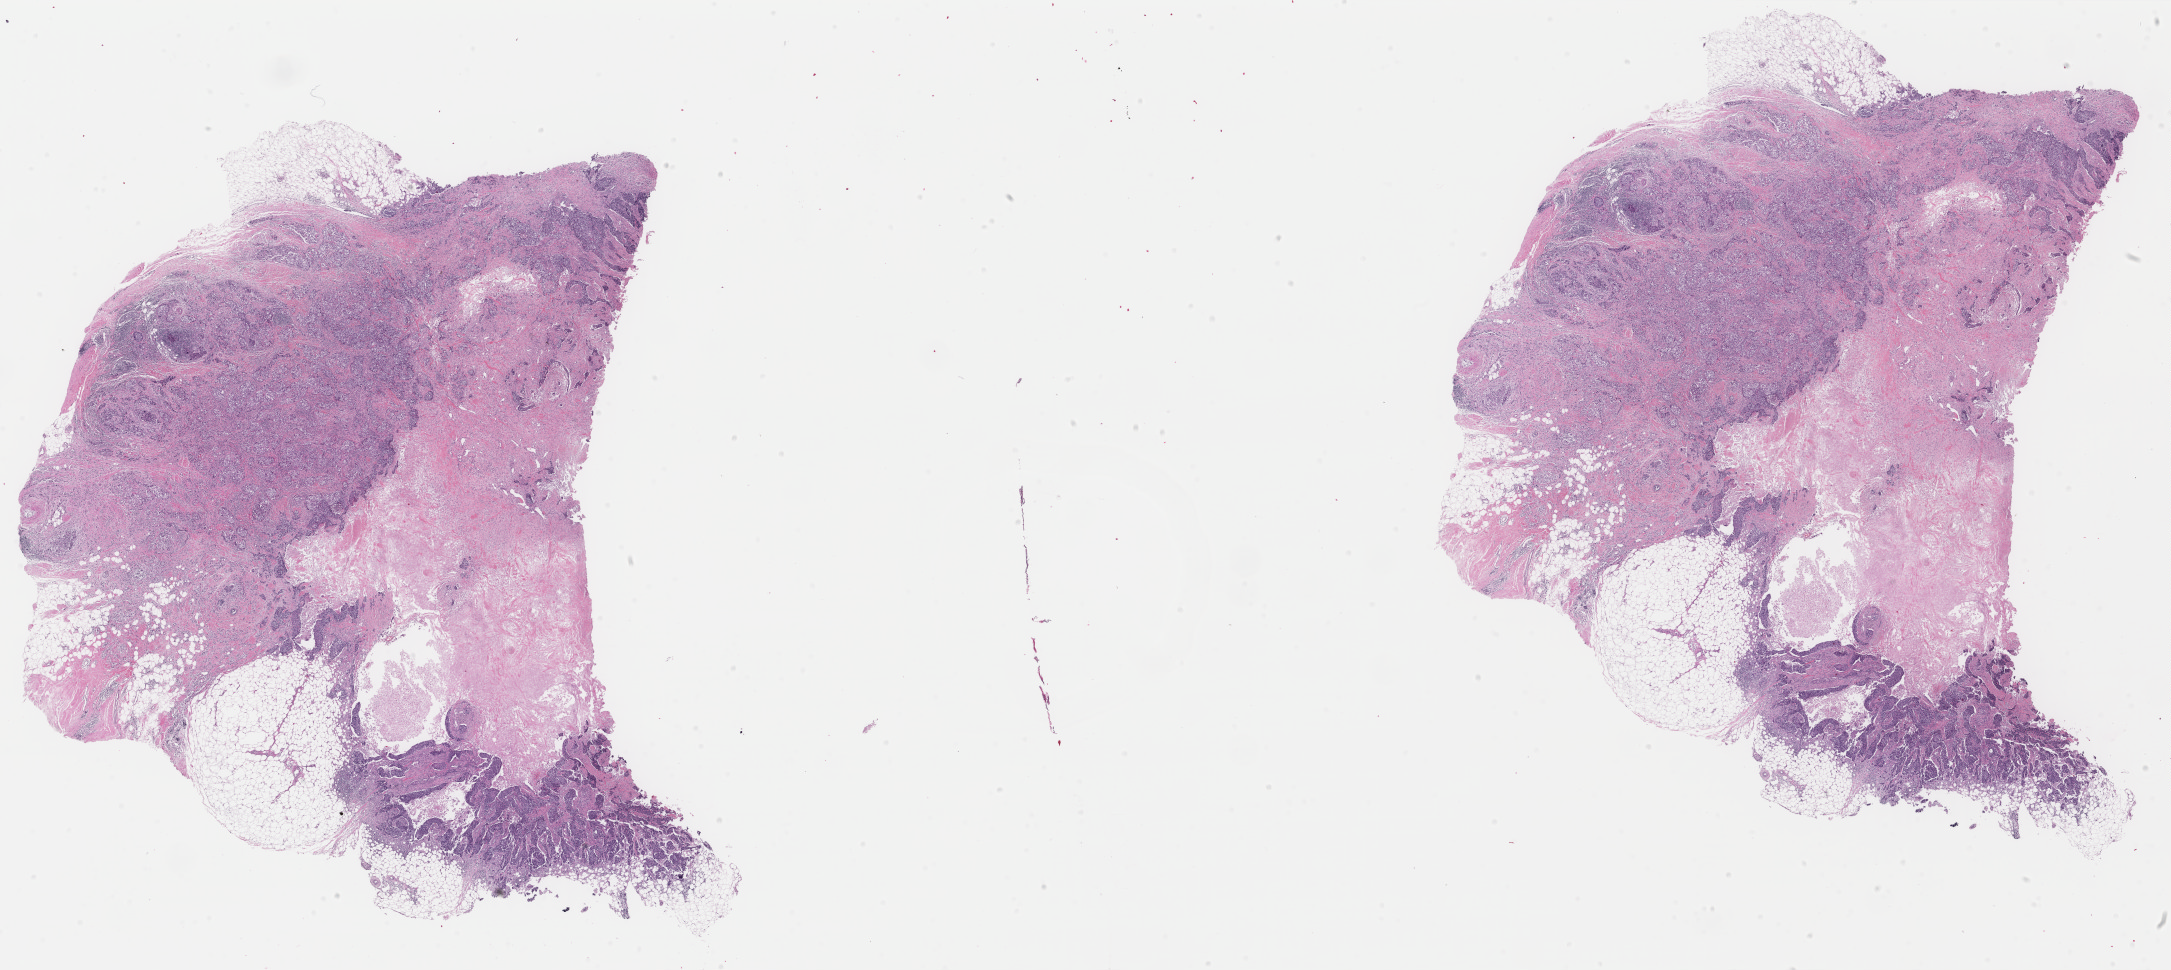
Digitized H&E tissue section (whole slide), low-resolution overview of the scanned area, about 34.5 x 15.4 mm (from a 40x scan); FFPE section; primary tumour sample from the breast. Patient: female, age at initial diagnosis 55 years.
Laterality: right. Diagnosis: Infiltrating duct carcinoma, NOS. AJCC pathologic stage: IIA.